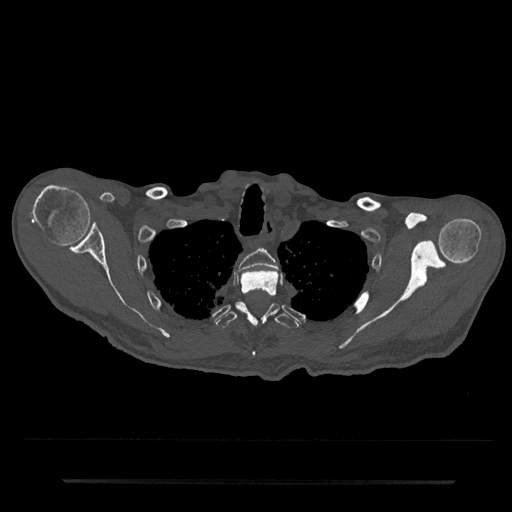
CT including the spine, one axial slice; position 650 of 797 along the scan axis; reconstruction kernel Br40s/3; 120 kVp; bone window (W 1800 / L 400 HU); 512 × 512 image matrix, field of view 427 × 427 mm. Male patient, age 74 years. Case-level facts recorded for this patient, not image findings: primary cancer: prostate.
Outlined on this slice (semi-automatic segmentation, software-assisted and operator-edited):
- T2 vertebra: bounding box [x1, y1, x2, y2] px = [239, 248, 277, 271]
- T3 vertebra: [240, 269, 279, 354]
- T4 vertebra: [216, 301, 299, 329]